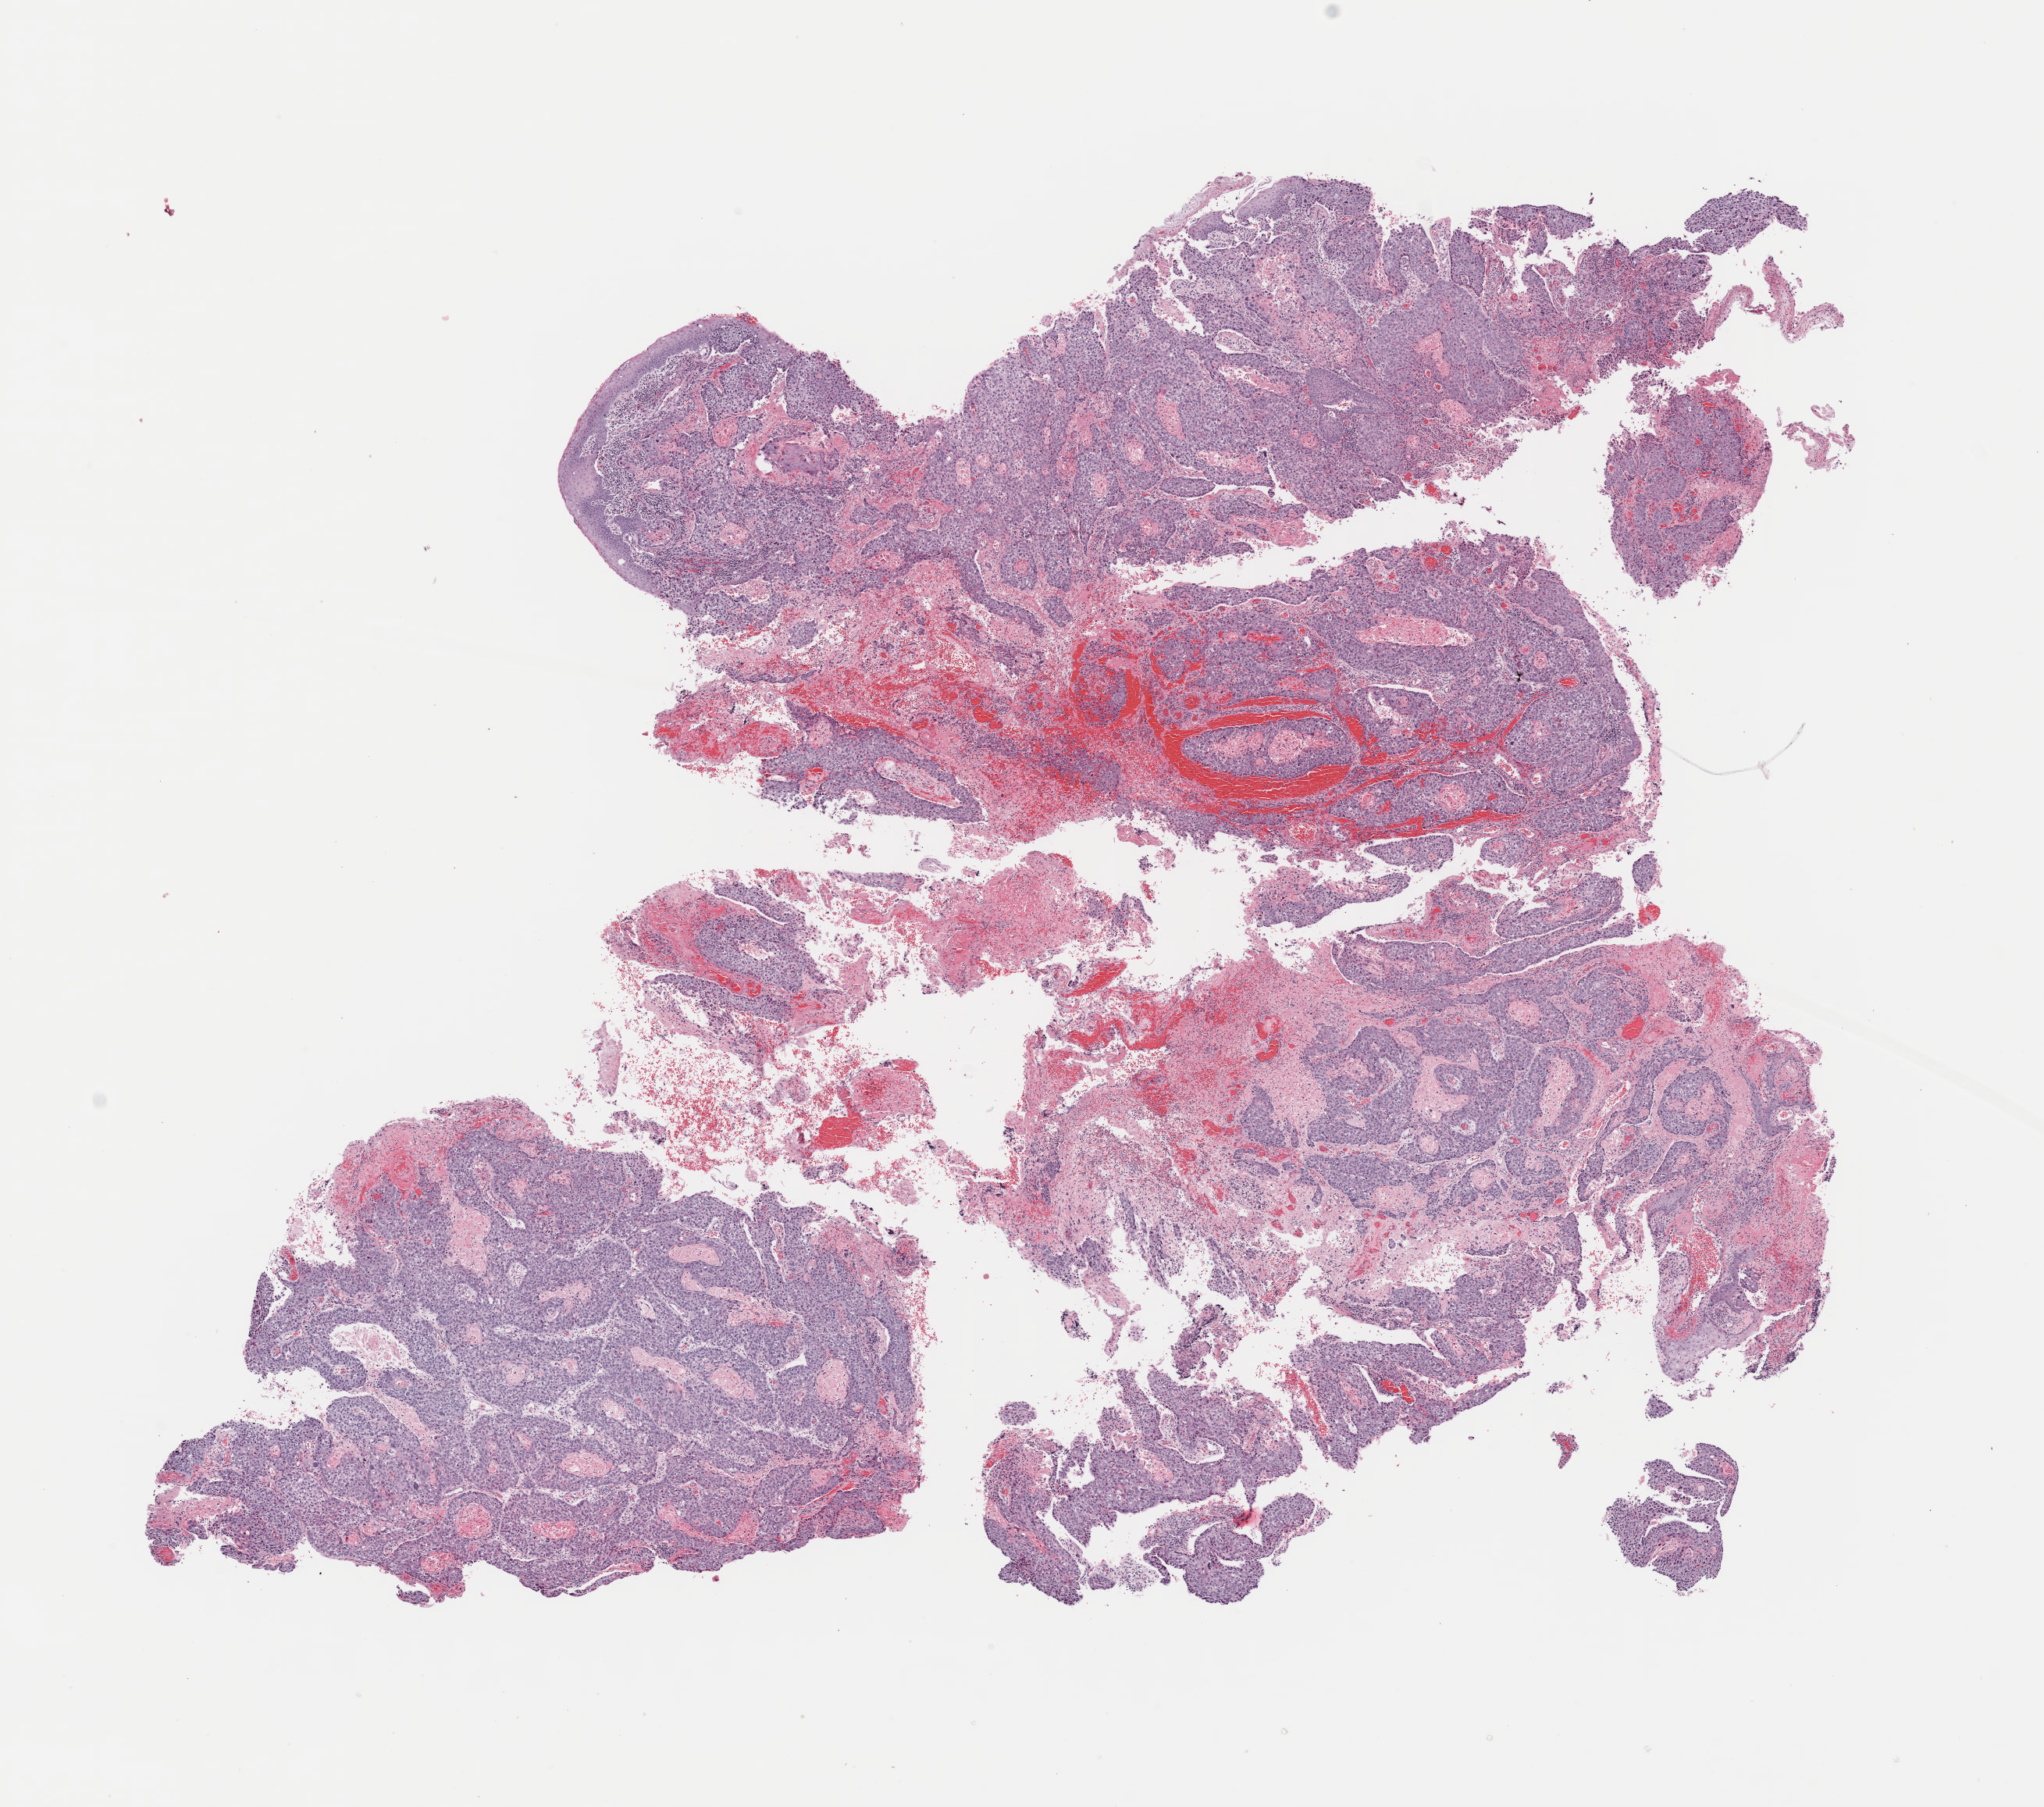
Whole-slide histology image, H&E-stained, shown as a low-resolution overview of the whole scanned area (about 10.3 x 9.1 mm, slide scanned at 40x); FFPE section; head and neck, primary tumour sample. Patient: male, age at initial diagnosis 50 years. Histologic grade: G3 (poorly differentiated).
AJCC pathologic stage: IVA (7th edition). Histologic diagnosis: Squamous cell carcinoma, NOS (larynx, NOS). TNM: T3 N2b MX.